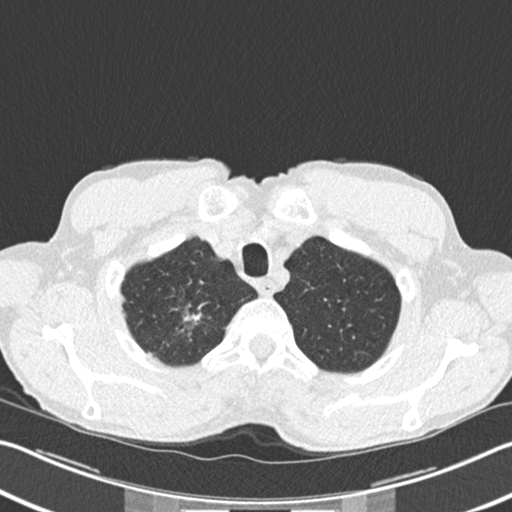
Low-dose screening chest CT, one axial slice. Slice 196 of 220 in the series (ordered by position). 120 kVp. Lung window (W 1500 / L -600 HU). 2 mm slice thickness. 512 × 512 image matrix, field of view 342 × 342 mm.
Structures marked on this image (outlined manually by an expert reader):
- lesion 1 (tumor, upper lobe of right lung): bounding box <183,313,202,325> (left, top, right, bottom; pixels)